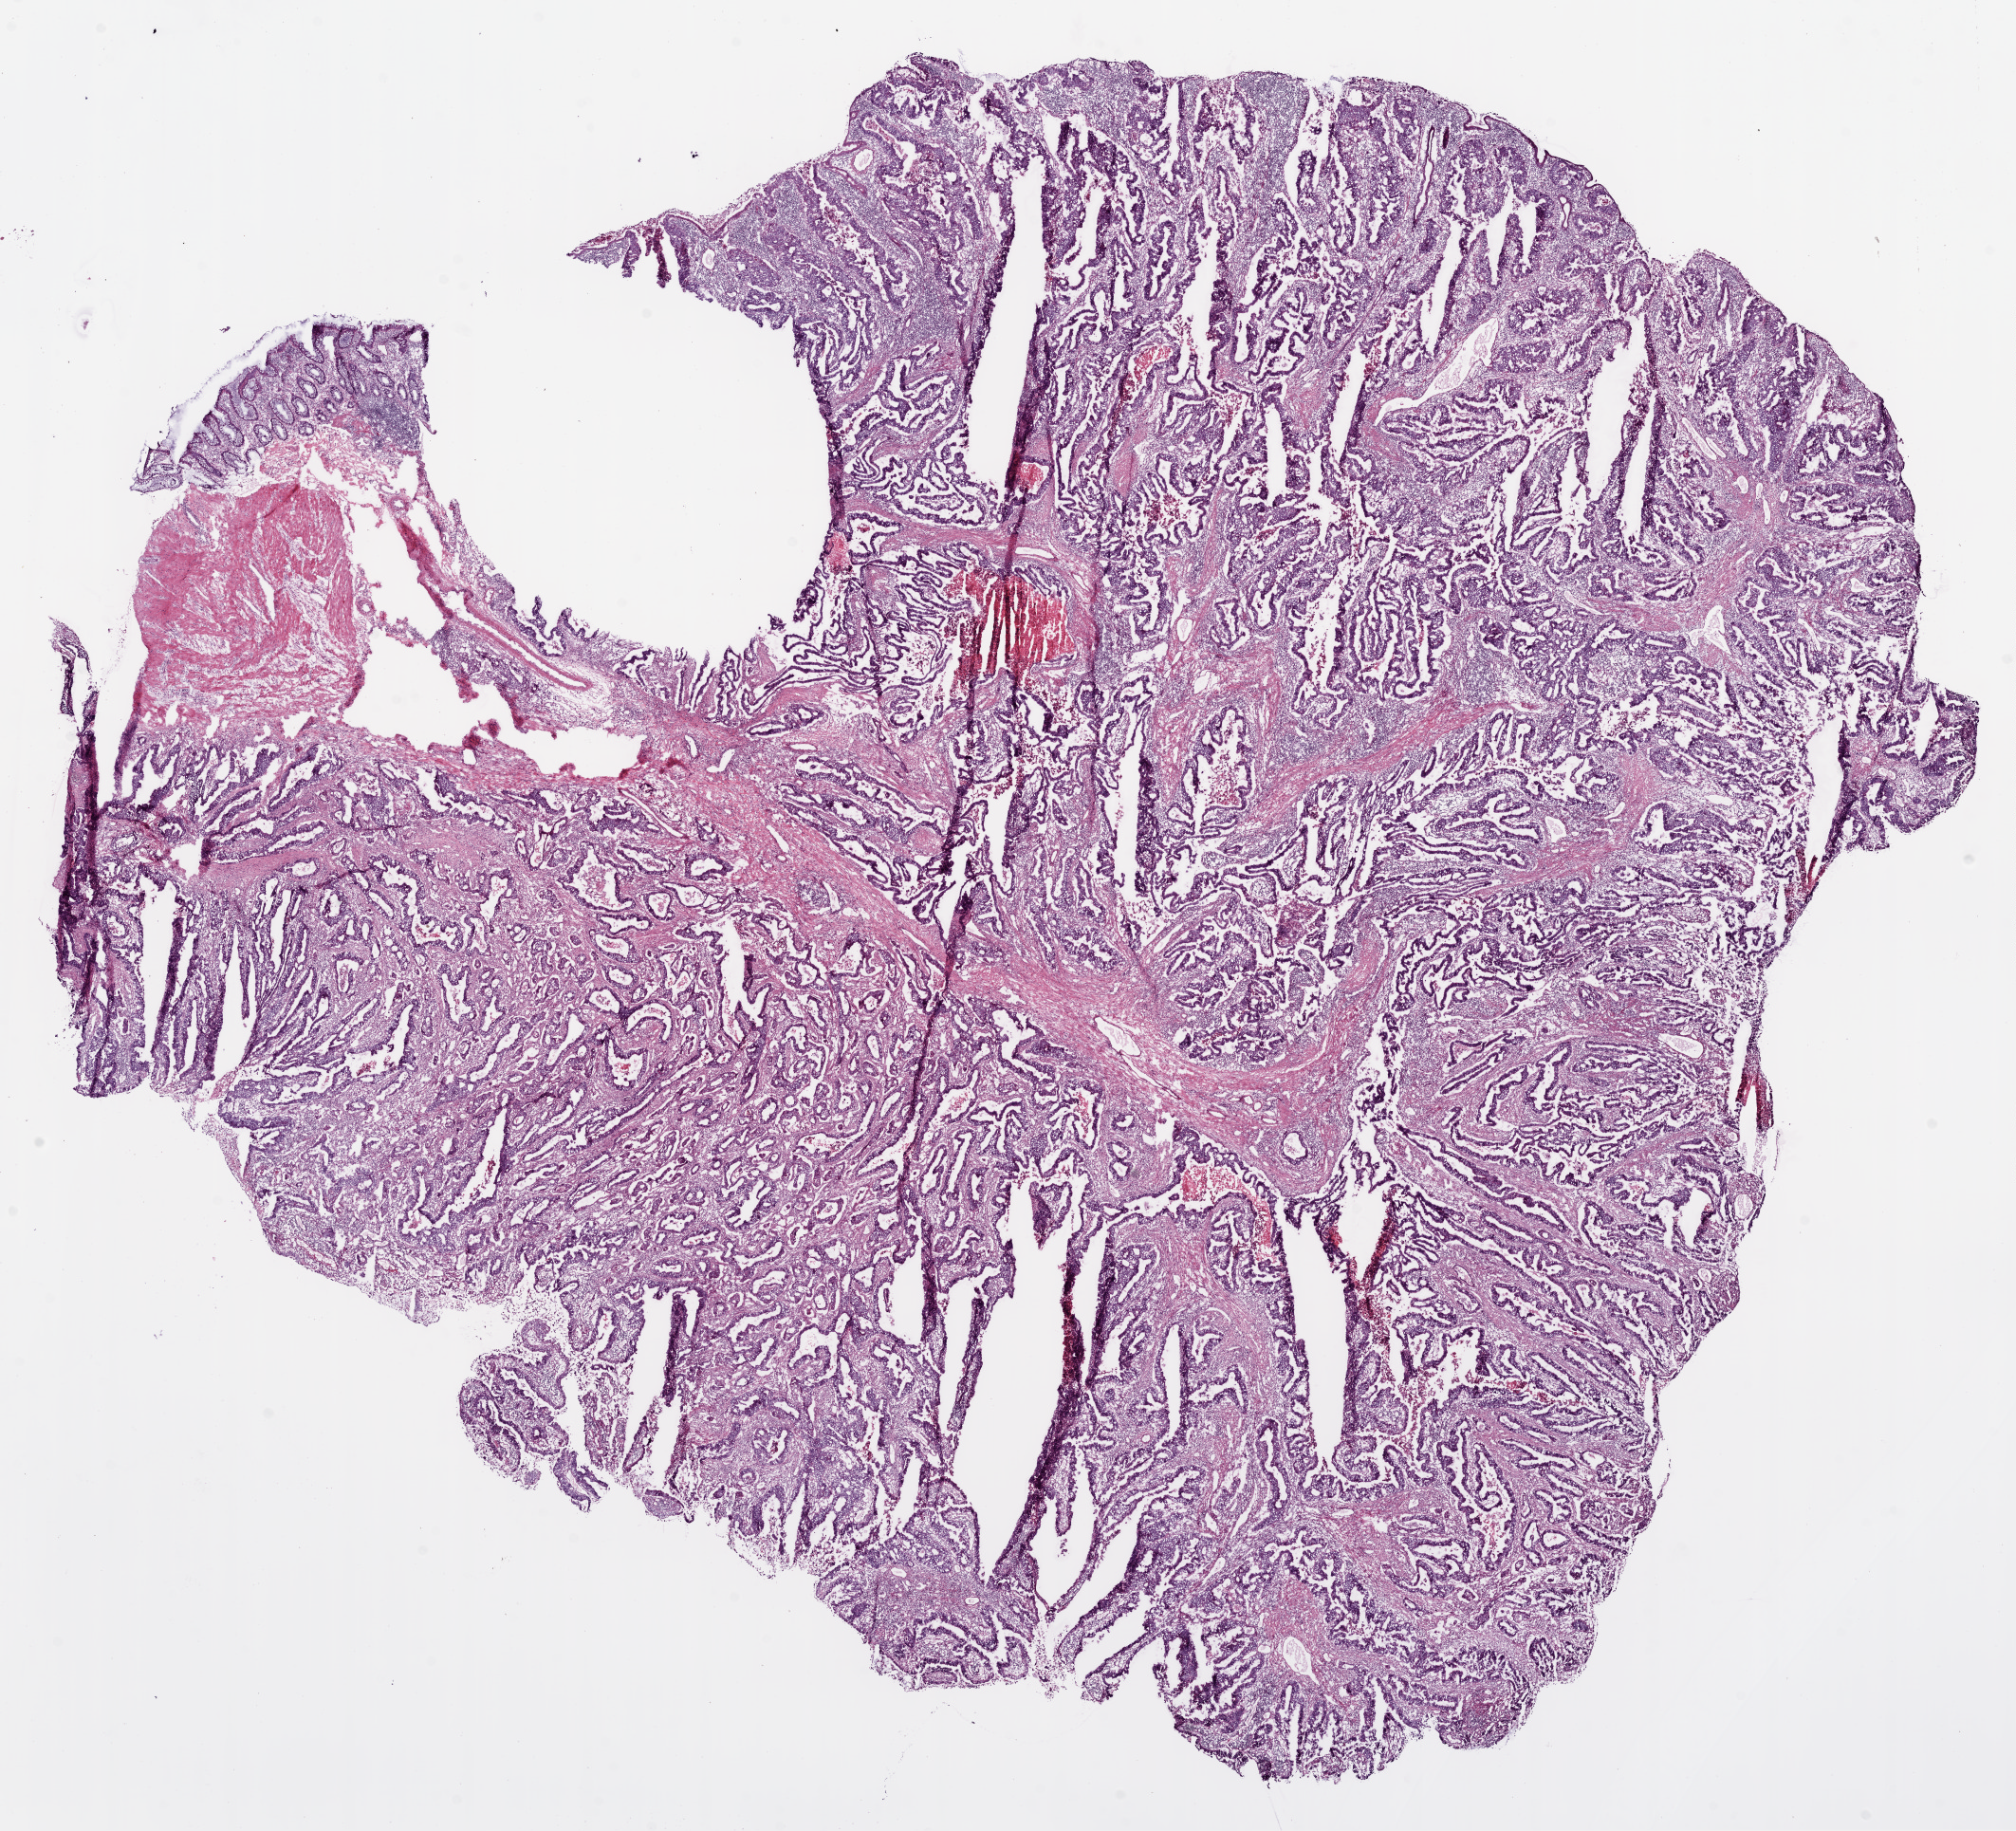
Whole-slide histology image, H&E — whole scanned area (about 17.1 x 15.5 mm, acquisition: 20x scan) shown as a low-resolution overview. Frozen section from the bottom of the tissue portion. Sample: primary tumour, colon. Patient: female, age at initial diagnosis 34 years. Slide review estimates, as recorded: tumour cells 65%, tumour nuclei 70%, normal cells 10%, stromal cells 15%, necrosis 10%.
AJCC pathologic stage: IIIA. Histologic diagnosis: Adenocarcinoma, NOS (rectosigmoid junction). Lymph nodes positive (case pathology): 2 of 52 examined. TNM: T1 N1b M0.